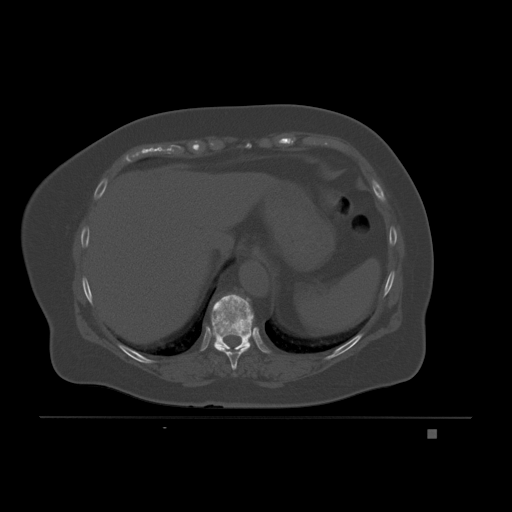
CT including the spine, one axial slice; position 104 of 221 along the scan axis; bone window (W 1800 / L 400 HU); 3 mm slice thickness; 512 × 512 image matrix. Female patient, age 63 years. From the clinical record (not read from this slice): primary cancer: breast.
Structures marked on this image (semi-automatic segmentation, software-assisted and operator-edited):
- T10 vertebra: bounding box <211,294,254,350> (left, top, right, bottom; pixels)
- T9 vertebra: <214,344,250,370>